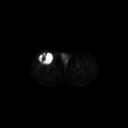
FDG PET of an extremity soft-tissue mass (from a PET/CT study), one axial slice. Position 277 of 311 along the scan axis. 3.27 mm slice thickness. 128 × 128 image matrix. Male patient, age 56 years. From the clinical record (not read from this slice): histological type: pleiomorphic leiomyosarcoma; grade: intermediate; site of the primary tumour: right thigh.
Outlined on this slice (expert contour drawn on MRI and transferred to this co-registered scan by the dataset authors):
- gross tumour volume including surrounding oedema: bounding box [x1, y1, x2, y2] px = [38, 53, 54, 65]
- gross tumour volume (mass): [38, 53, 54, 65]